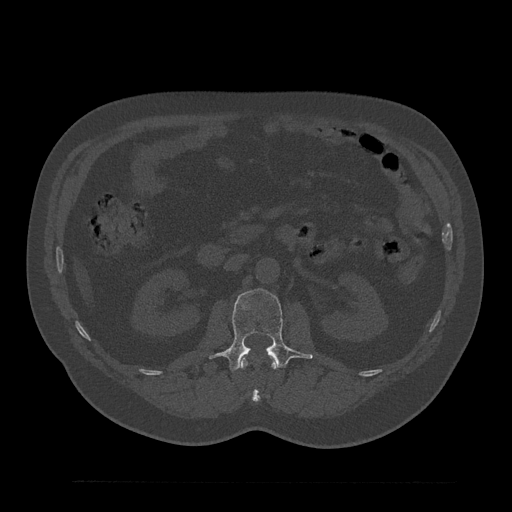
CT including the spine, one axial slice. Slice 114 of 797 in the series (ordered by position). Reconstruction kernel Br40s/3. 120 kVp. Bone window (W 1800 / L 400 HU). 0.5 mm slice thickness. 512 × 512 image matrix, field of view 430 × 430 mm. Male patient, age 61 years. From the clinical record (not read from this slice): primary cancer: prostate.
Annotated regions visible in this slice (semi-automatic segmentation, software-assisted and operator-edited):
- L1 vertebra: bounding box [x1, y1, x2, y2] px = [241, 353, 277, 403]
- L2 vertebra: [210, 288, 312, 372]